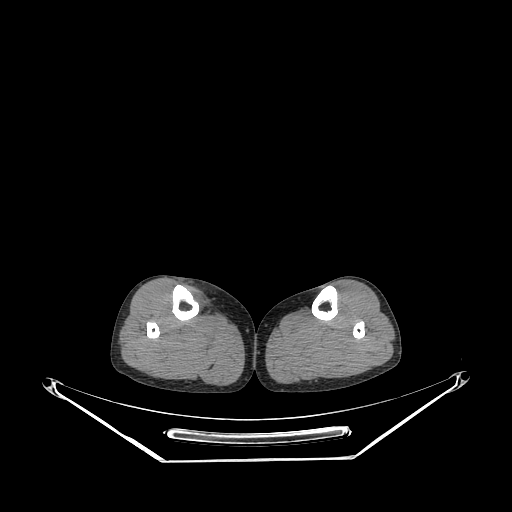
CT of an extremity soft-tissue mass (from a PET/CT study), one axial slice. Position 133 of 267 along the scan axis. 140 kVp. Soft-tissue window (W 400 / L 40 HU). 3.75 mm slice thickness. 512 × 512 image matrix, field of view 500 × 500 mm. Female patient. Case-level facts recorded for this patient, not image findings: histological type: undifferentiated – high grade; grade: high; site of the primary tumour: right thigh.
Annotated regions visible in this slice (expert contour drawn on MRI and transferred to this co-registered scan by the dataset authors):
- gross tumour volume (mass): bounding box [x1, y1, x2, y2] px = [185, 285, 207, 309]